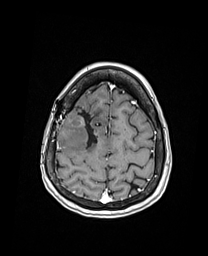
Brain MRI from a brain-tumour surgery series, one axial slice. Position 43 of 192 along the scan axis. T1-weighted post-contrast. 1 mm slice thickness. 208 × 256 image matrix, field of view 208 × 256 mm. Case-level facts recorded for this patient, not image findings: histopathology: Oligodendroglioma; WHO grade: 3.
Structures marked on this image (outlined manually by an expert reader):
- previous resection cavity: bounding box <72,109,99,148> (left, top, right, bottom; pixels)